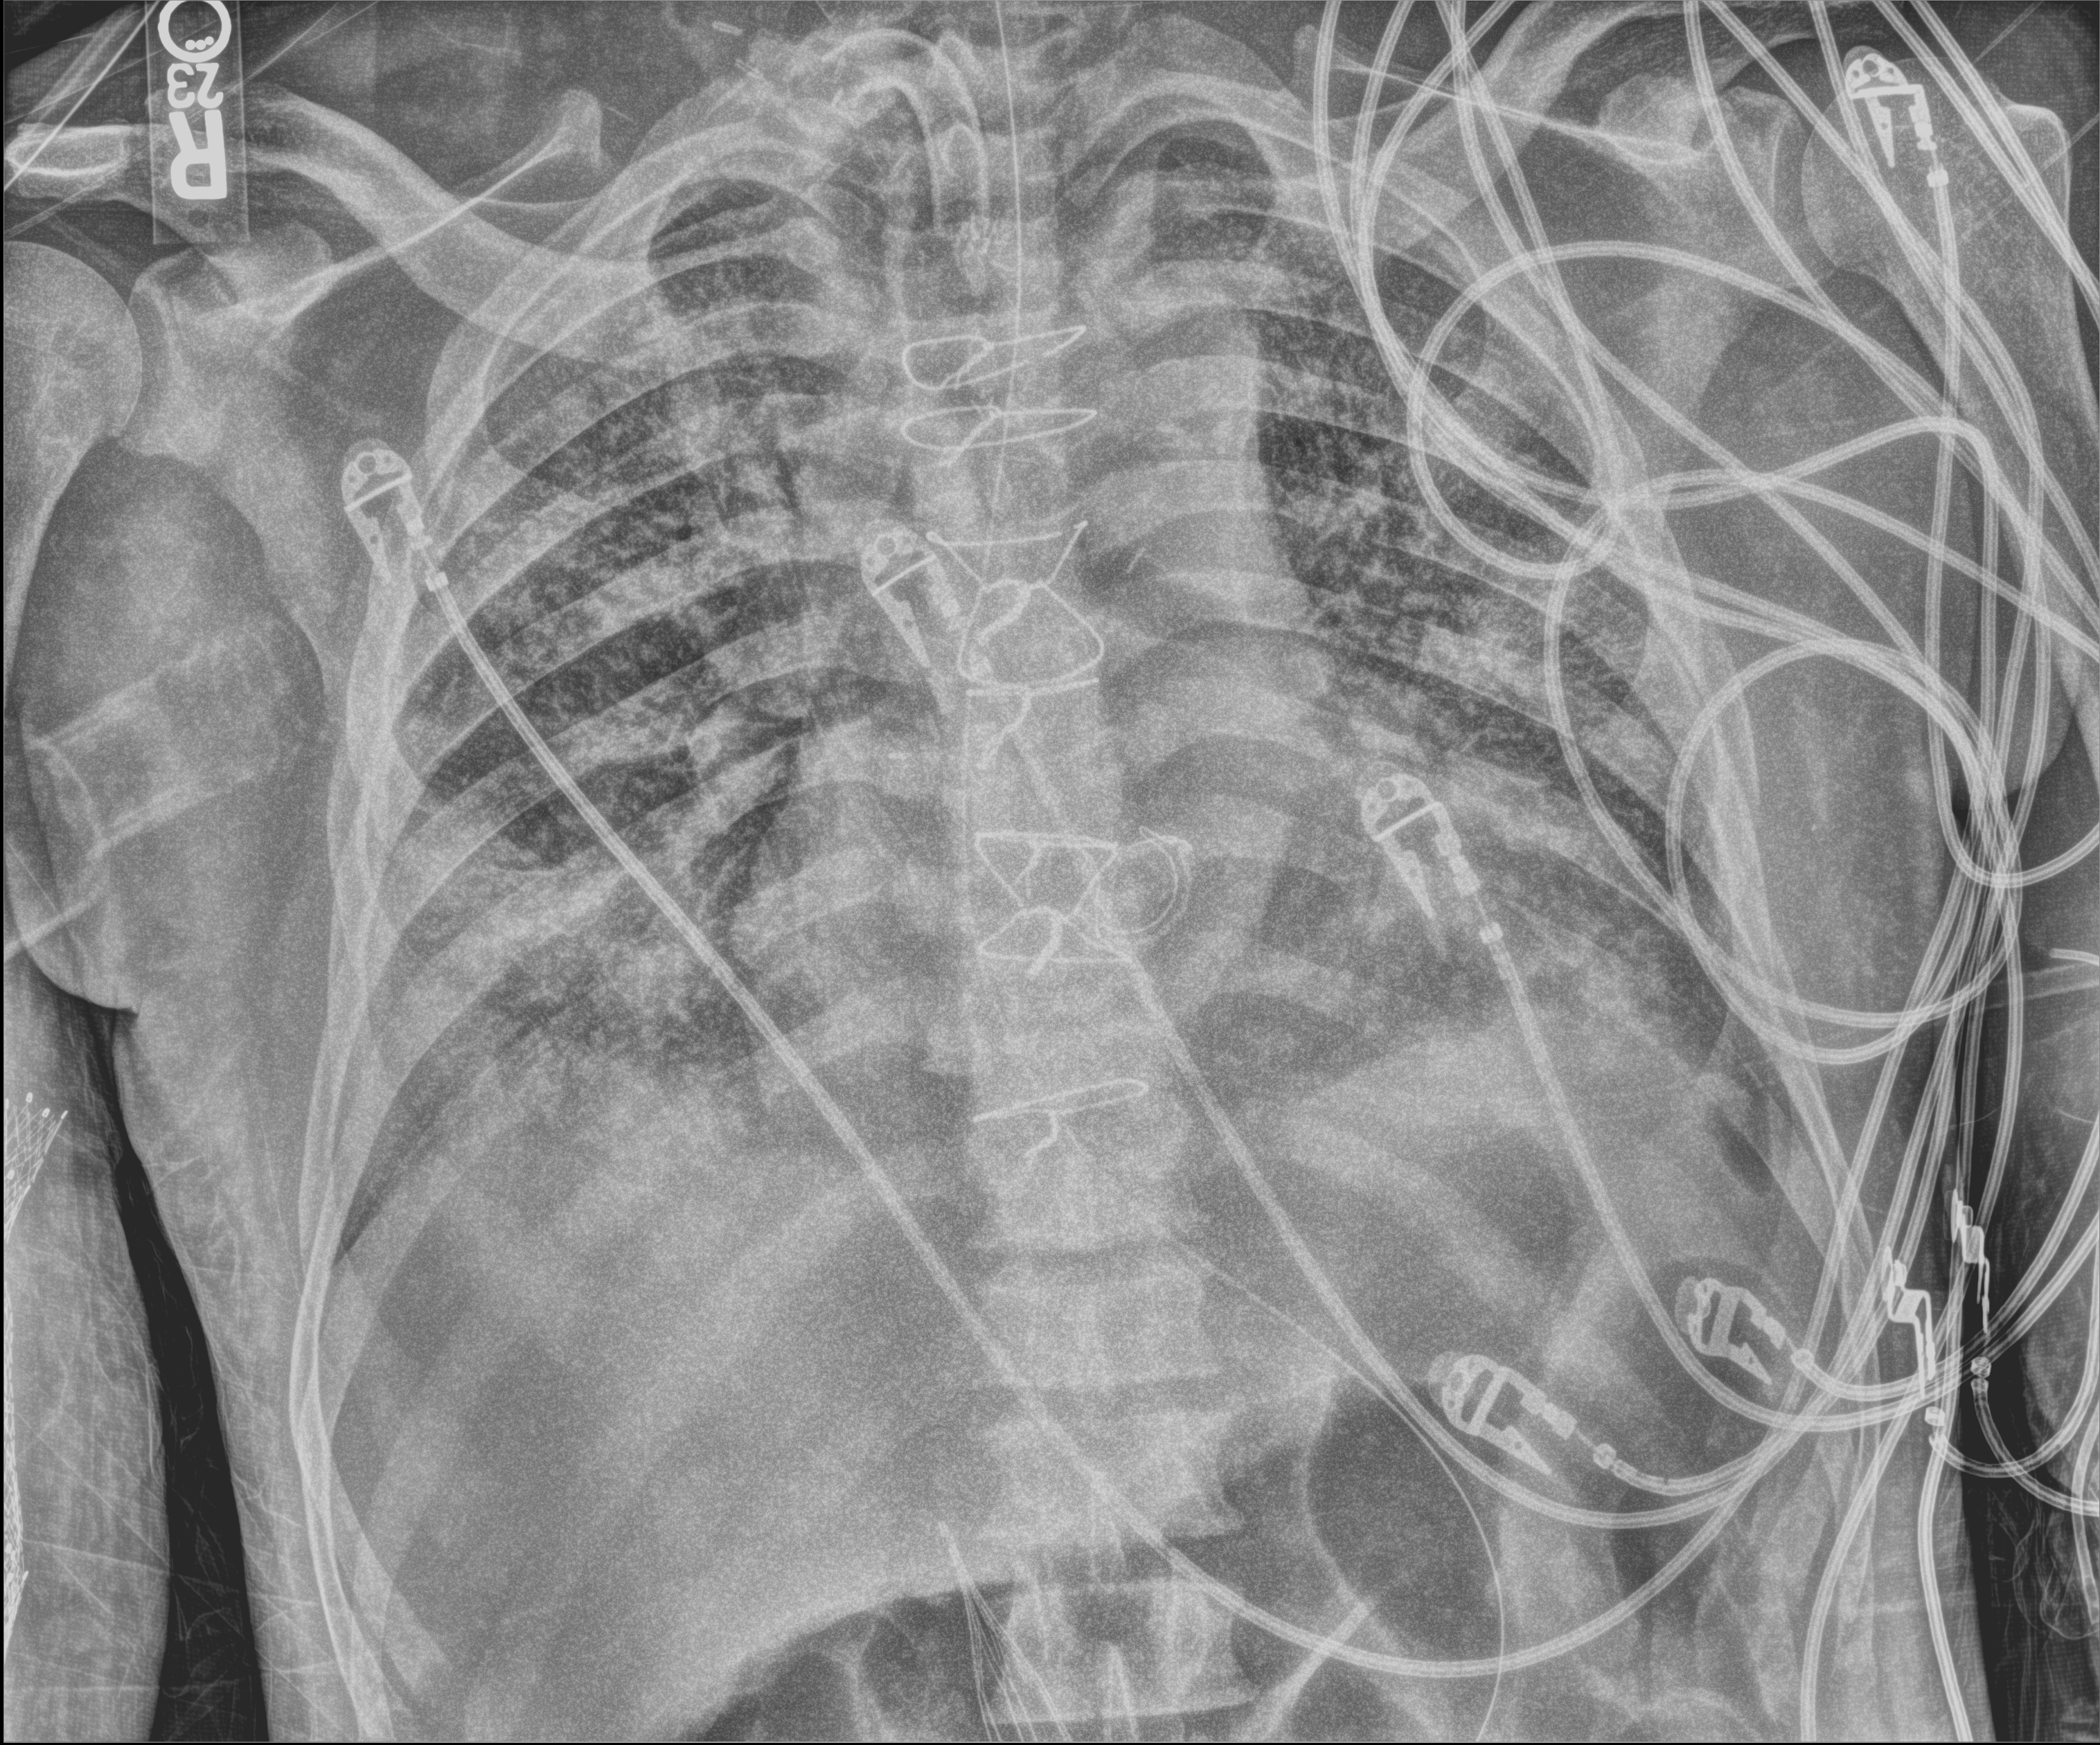
Bedside chest radiograph (digital radiography); anteroposterior (AP) projection. Male patient hospitalised with COVID-19, age 60–74 years.
Admission-level facts for this patient (not findings on this image; timing relative to this image not recorded):
- chronic kidney disease (admission record): no
- mechanically ventilated during this hospital stay: yes